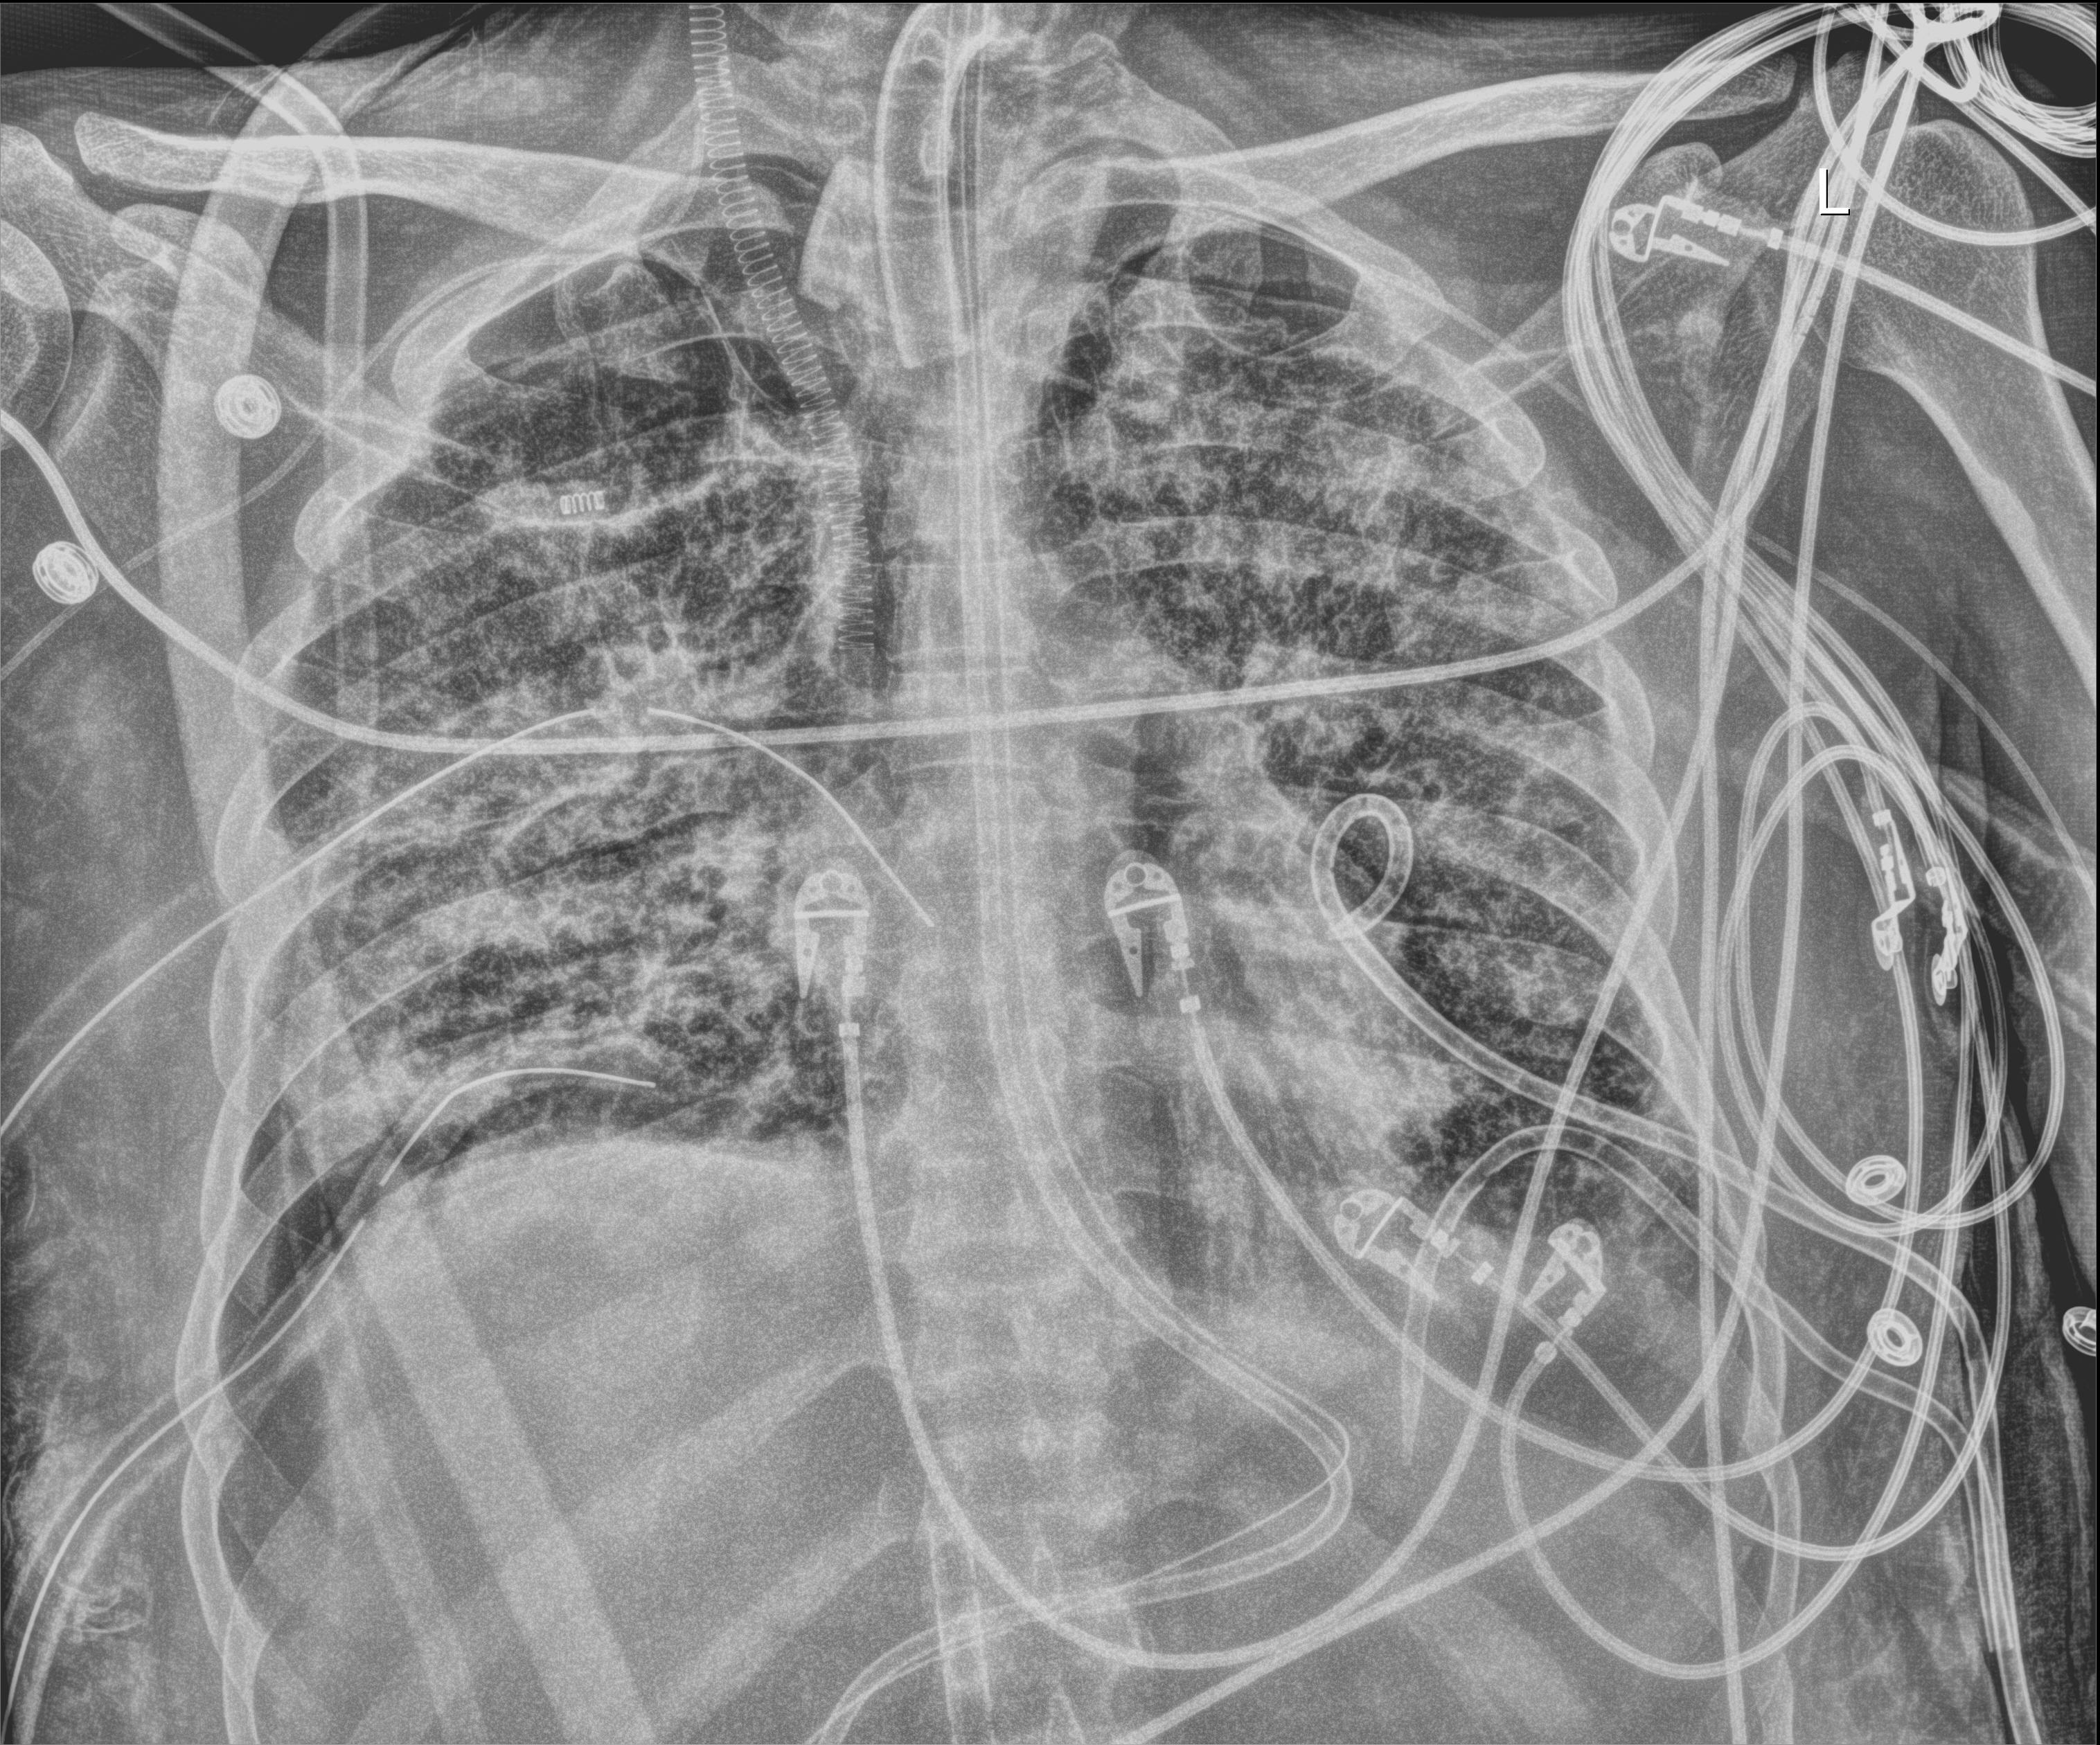
Portable chest radiograph; anteroposterior (AP) projection. Patient hospitalised with COVID-19, aged 18–59 years.
Admission-level facts for this patient (not findings on this image; timing relative to this image not recorded):
- hypertension (admission record): no
- admitted to intensive care during this hospital stay: yes
- mechanically ventilated during this hospital stay: yes